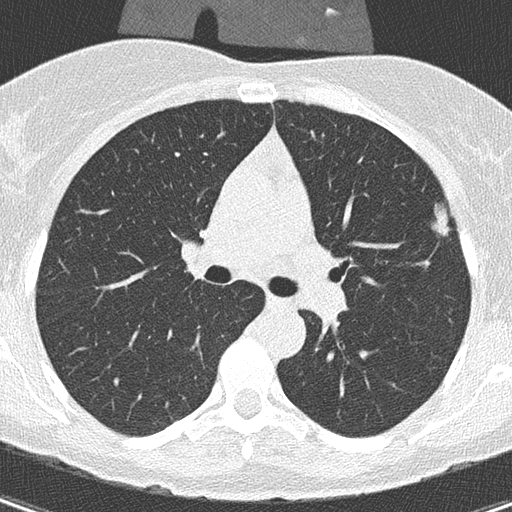
Chest CT (low-dose screening protocol), one axial image, baseline annual screen, lung window (W 1500 / L -600 HU), 120 kVp. Female, age 56 years at enrolment. Former smoker at enrolment.
Lesion marked by an expert reader, bounding box <421,193,467,248> (left, top, right, bottom; pixels). Screening reader's record for this exam (one nodule recorded; not confirmed to be the boxed lesion): non-calcified nodule or mass ≥4 mm, left upper lobe, 110 × 106 mm, spiculated (stellate) margins, soft tissue attenuation. Official screen result: positive, change unspecified: nodule(s) >= 4 mm or enlarging nodule(s), mass(es), or other non-specific abnormalities suspicious for lung cancer. Participant outcome: lung cancer diagnosed 417 days after this screen (after the second annual screen) — adenocarcinoma, NOS, left upper lobe, moderately differentiated (G2), stage IA (AJCC 6th edition), 11 mm at pathology.